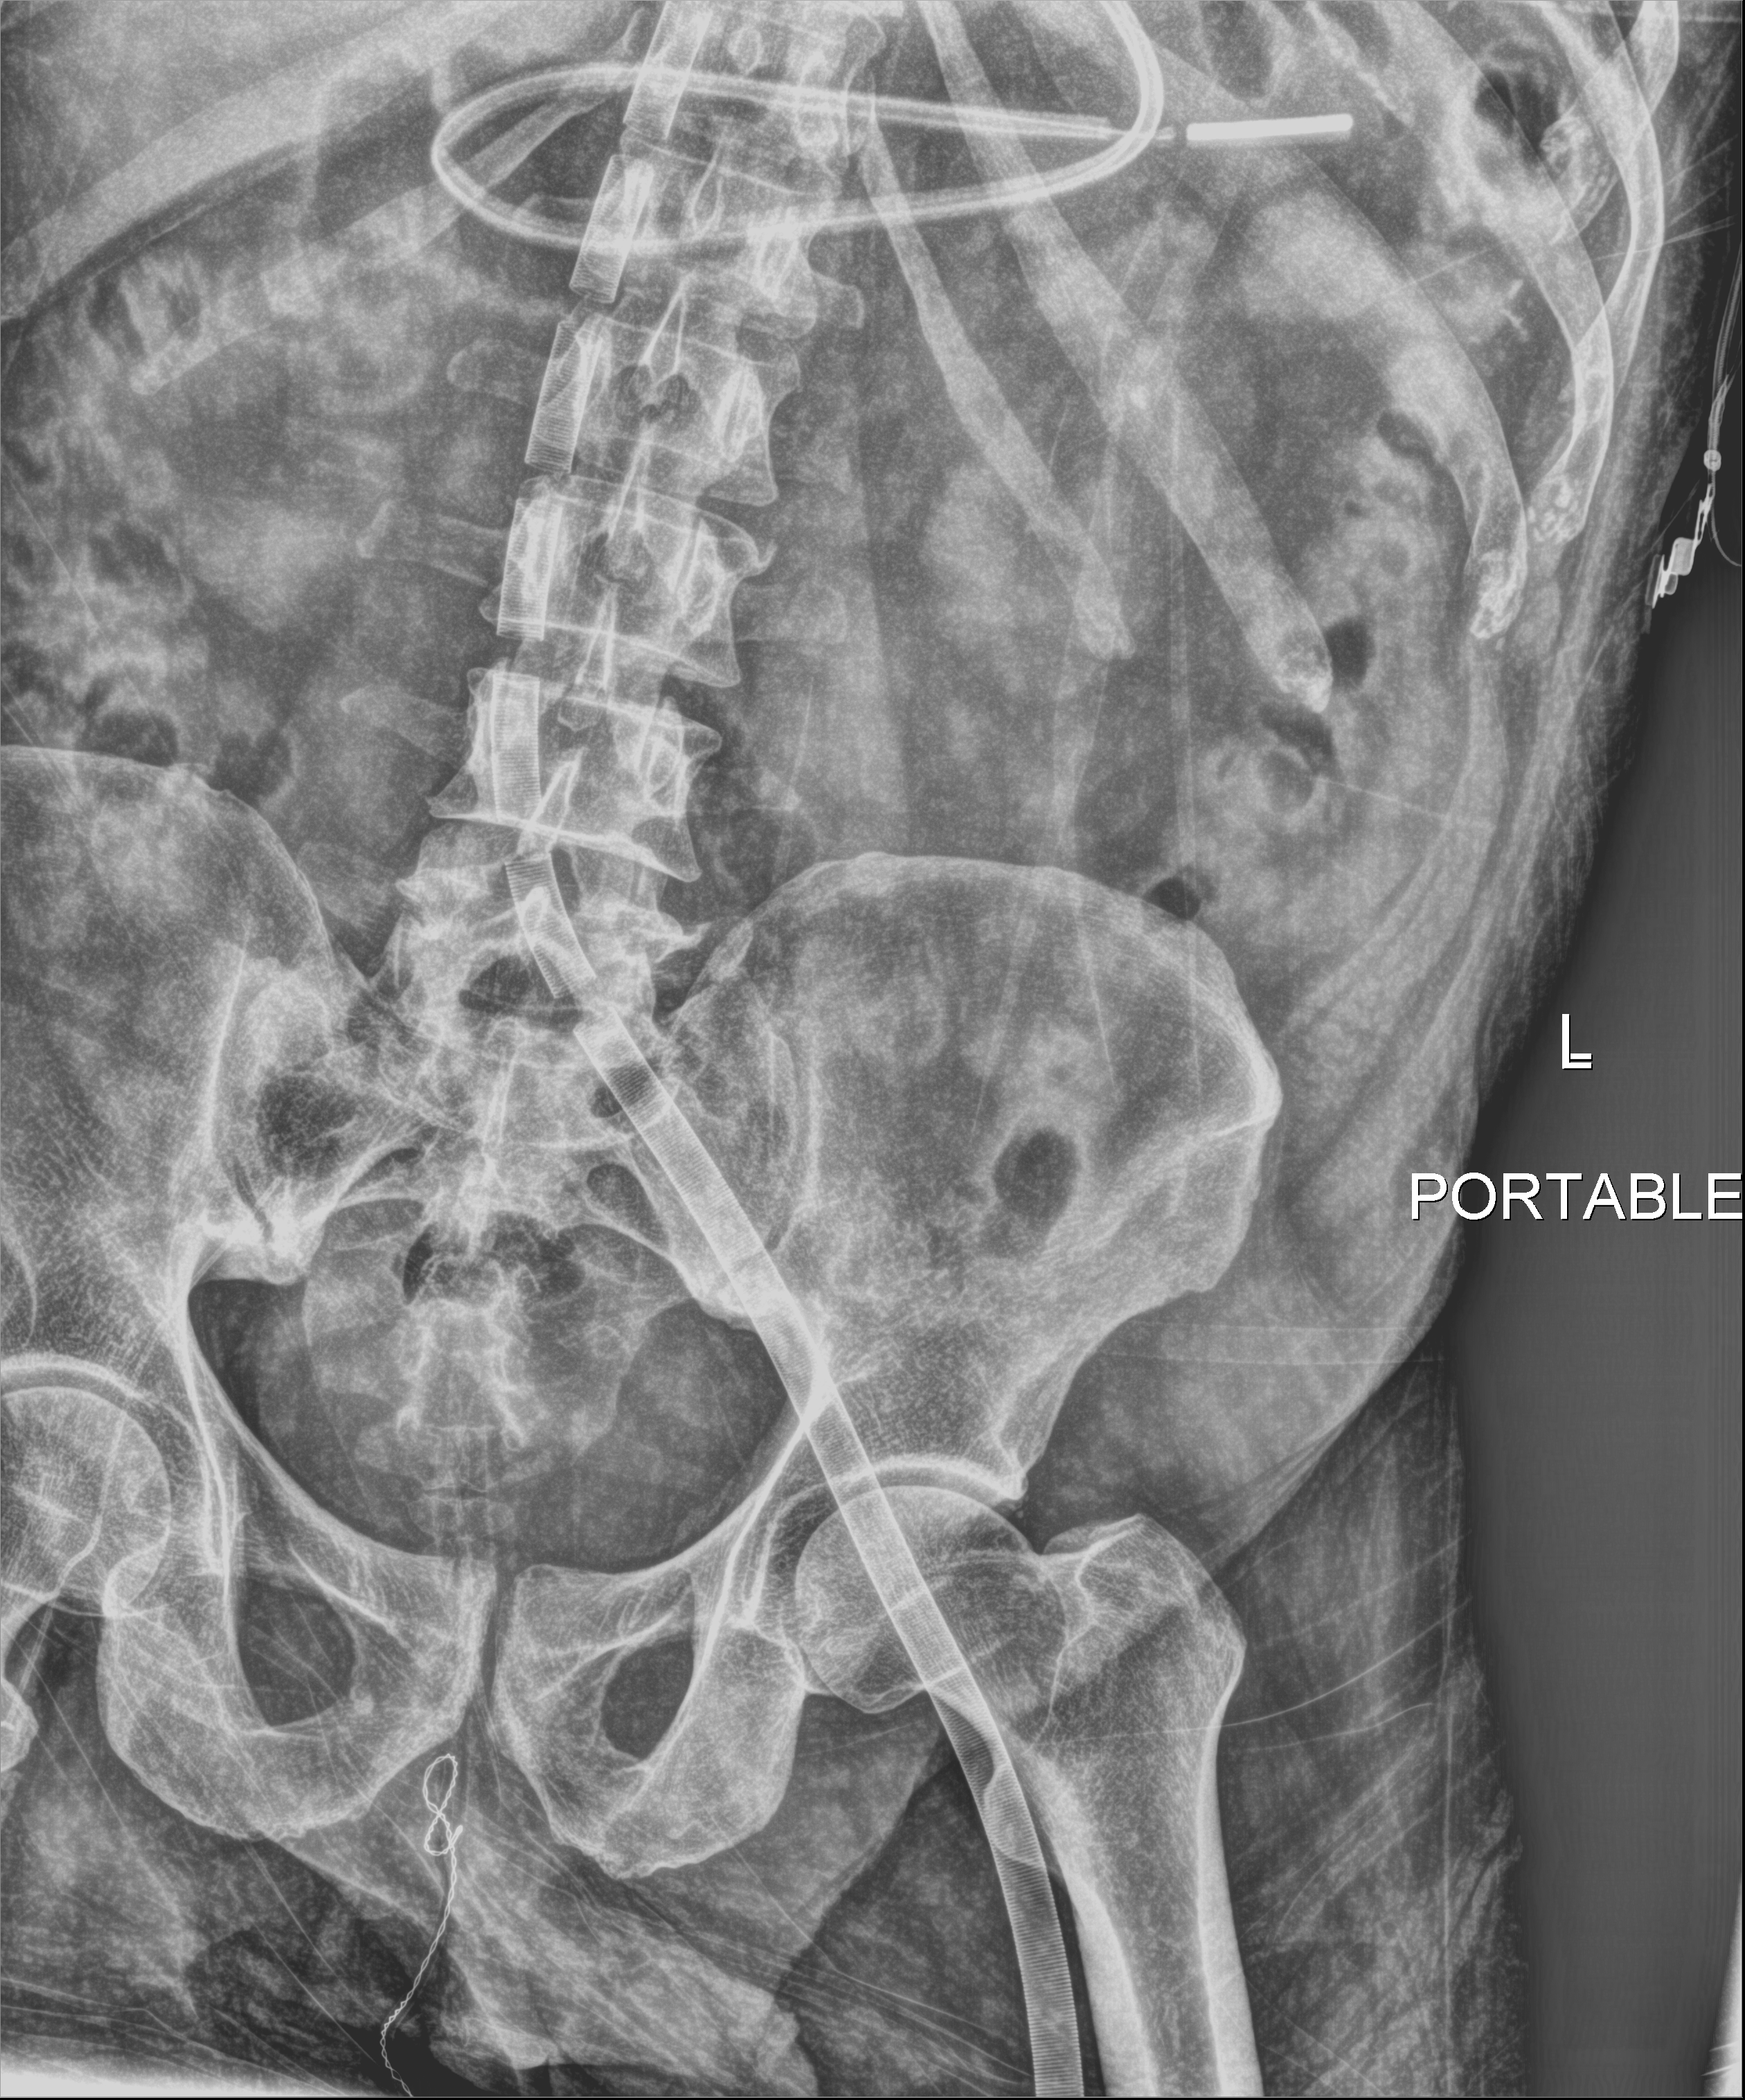
Abdomen X-ray (portable). Patient hospitalised with COVID-19; male, aged 18–59 years.
From the hospital-stay record, not from the radiograph (when in the stay this image was taken is not recorded):
- diabetes (admission record): no
- mechanically ventilated during this hospital stay: yes